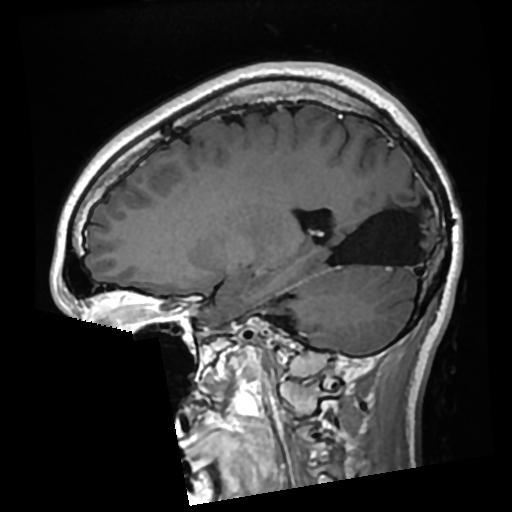
Brain MRI from a brain-tumour surgery series, one sagittal slice. Slice 109 of 276 in the series (ordered by position). T1-weighted post-contrast. 0.7 mm slice thickness. 512 × 512 image matrix, field of view 250 × 250 mm. From the clinical record (not read from this slice): histopathology: Glioma with ependymal features; WHO grade: 2; tumour location: Left Parietal.
Outlined on this slice (manually delineated by an expert):
- previous resection cavity: bounding box (x1, y1, x2, y2) in pixels: (330, 186, 422, 266)